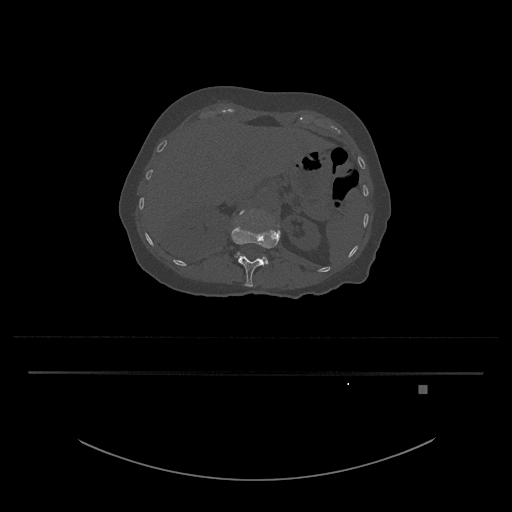
CT including the spine, one axial slice; reconstruction kernel Br40s/3; 120 kVp; bone window (W 1800 / L 400 HU); 0.5 mm slice thickness; 512 × 512 image matrix, field of view 500 × 500 mm. Patient: female, 57 years. Case-level facts recorded for this patient, not image findings: primary cancer: cervical.
Outlined on this slice (semi-automatically segmented with operator editing):
- L1 vertebra: bounding box [x1, y1, x2, y2] px = [231, 222, 281, 287]